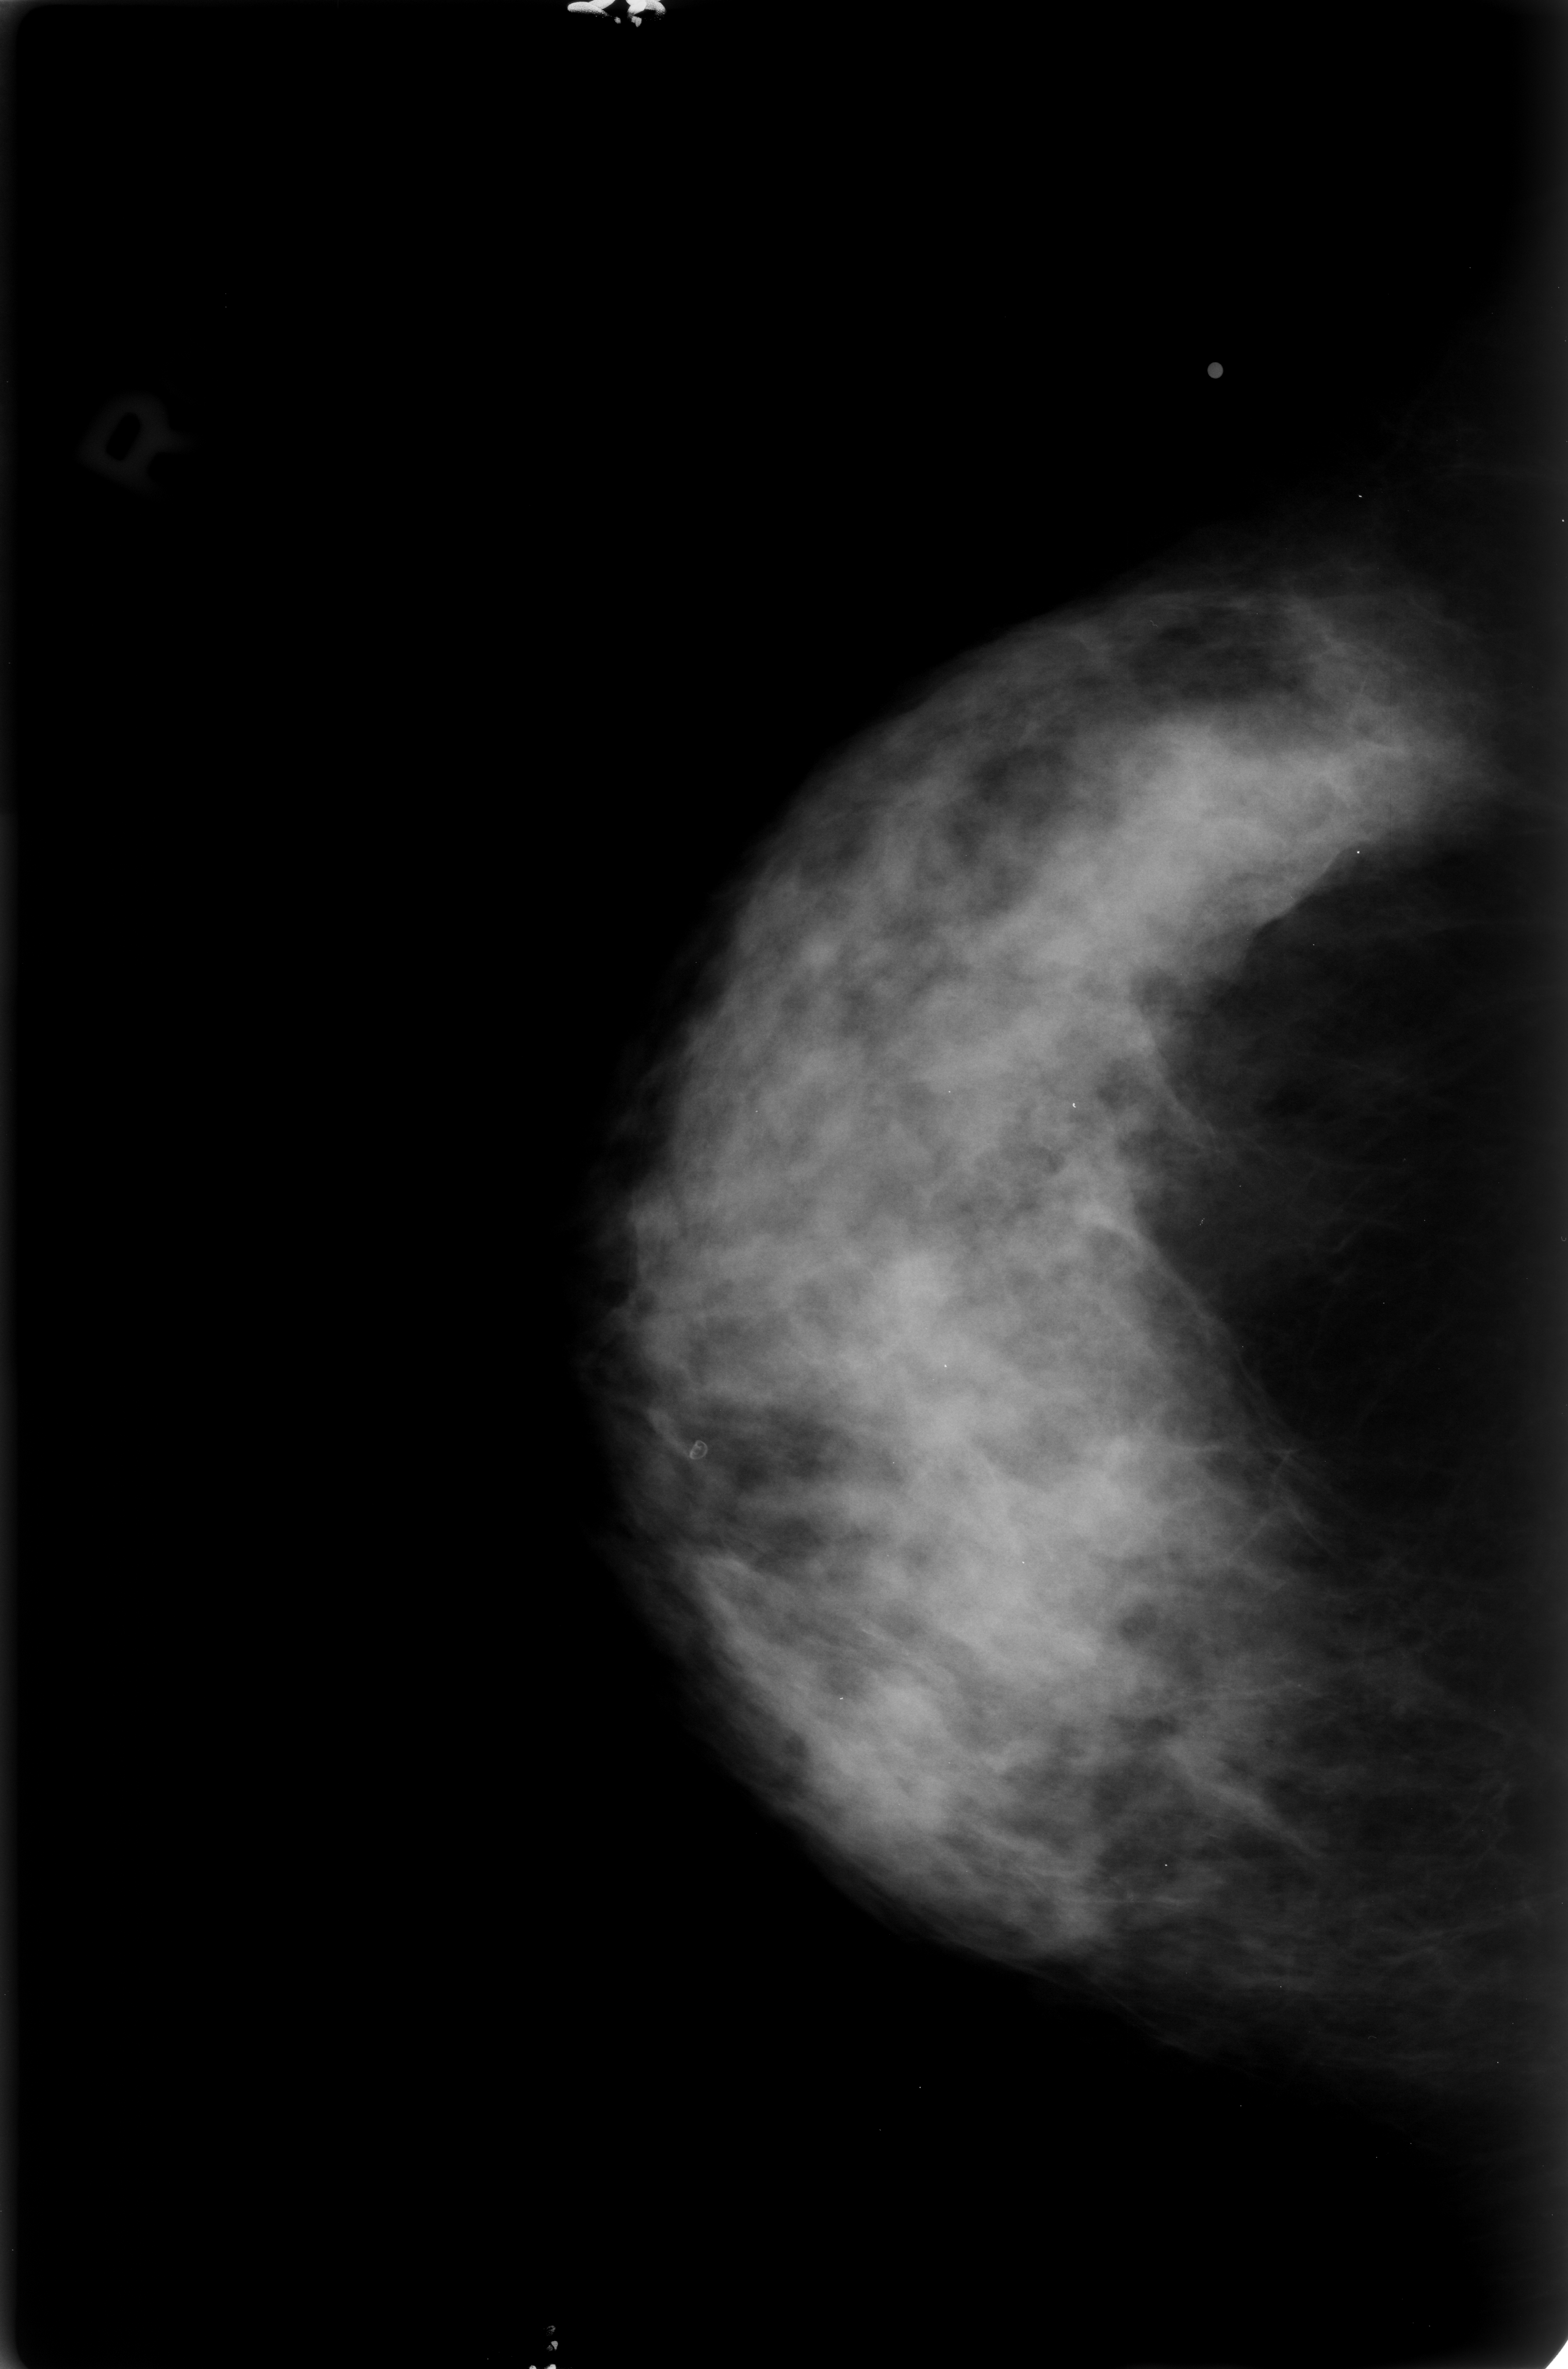
Scanned film-screen mammogram; right breast; CC view; BI-RADS breast density category 4 (scale 1–4).
Marked abnormality: calcifications, morphology lucent center; BI-RADS assessment category 2; subtlety rating 3 on a 1 (subtle) to 5 (obvious) scale; benign without callback (not worked up further).